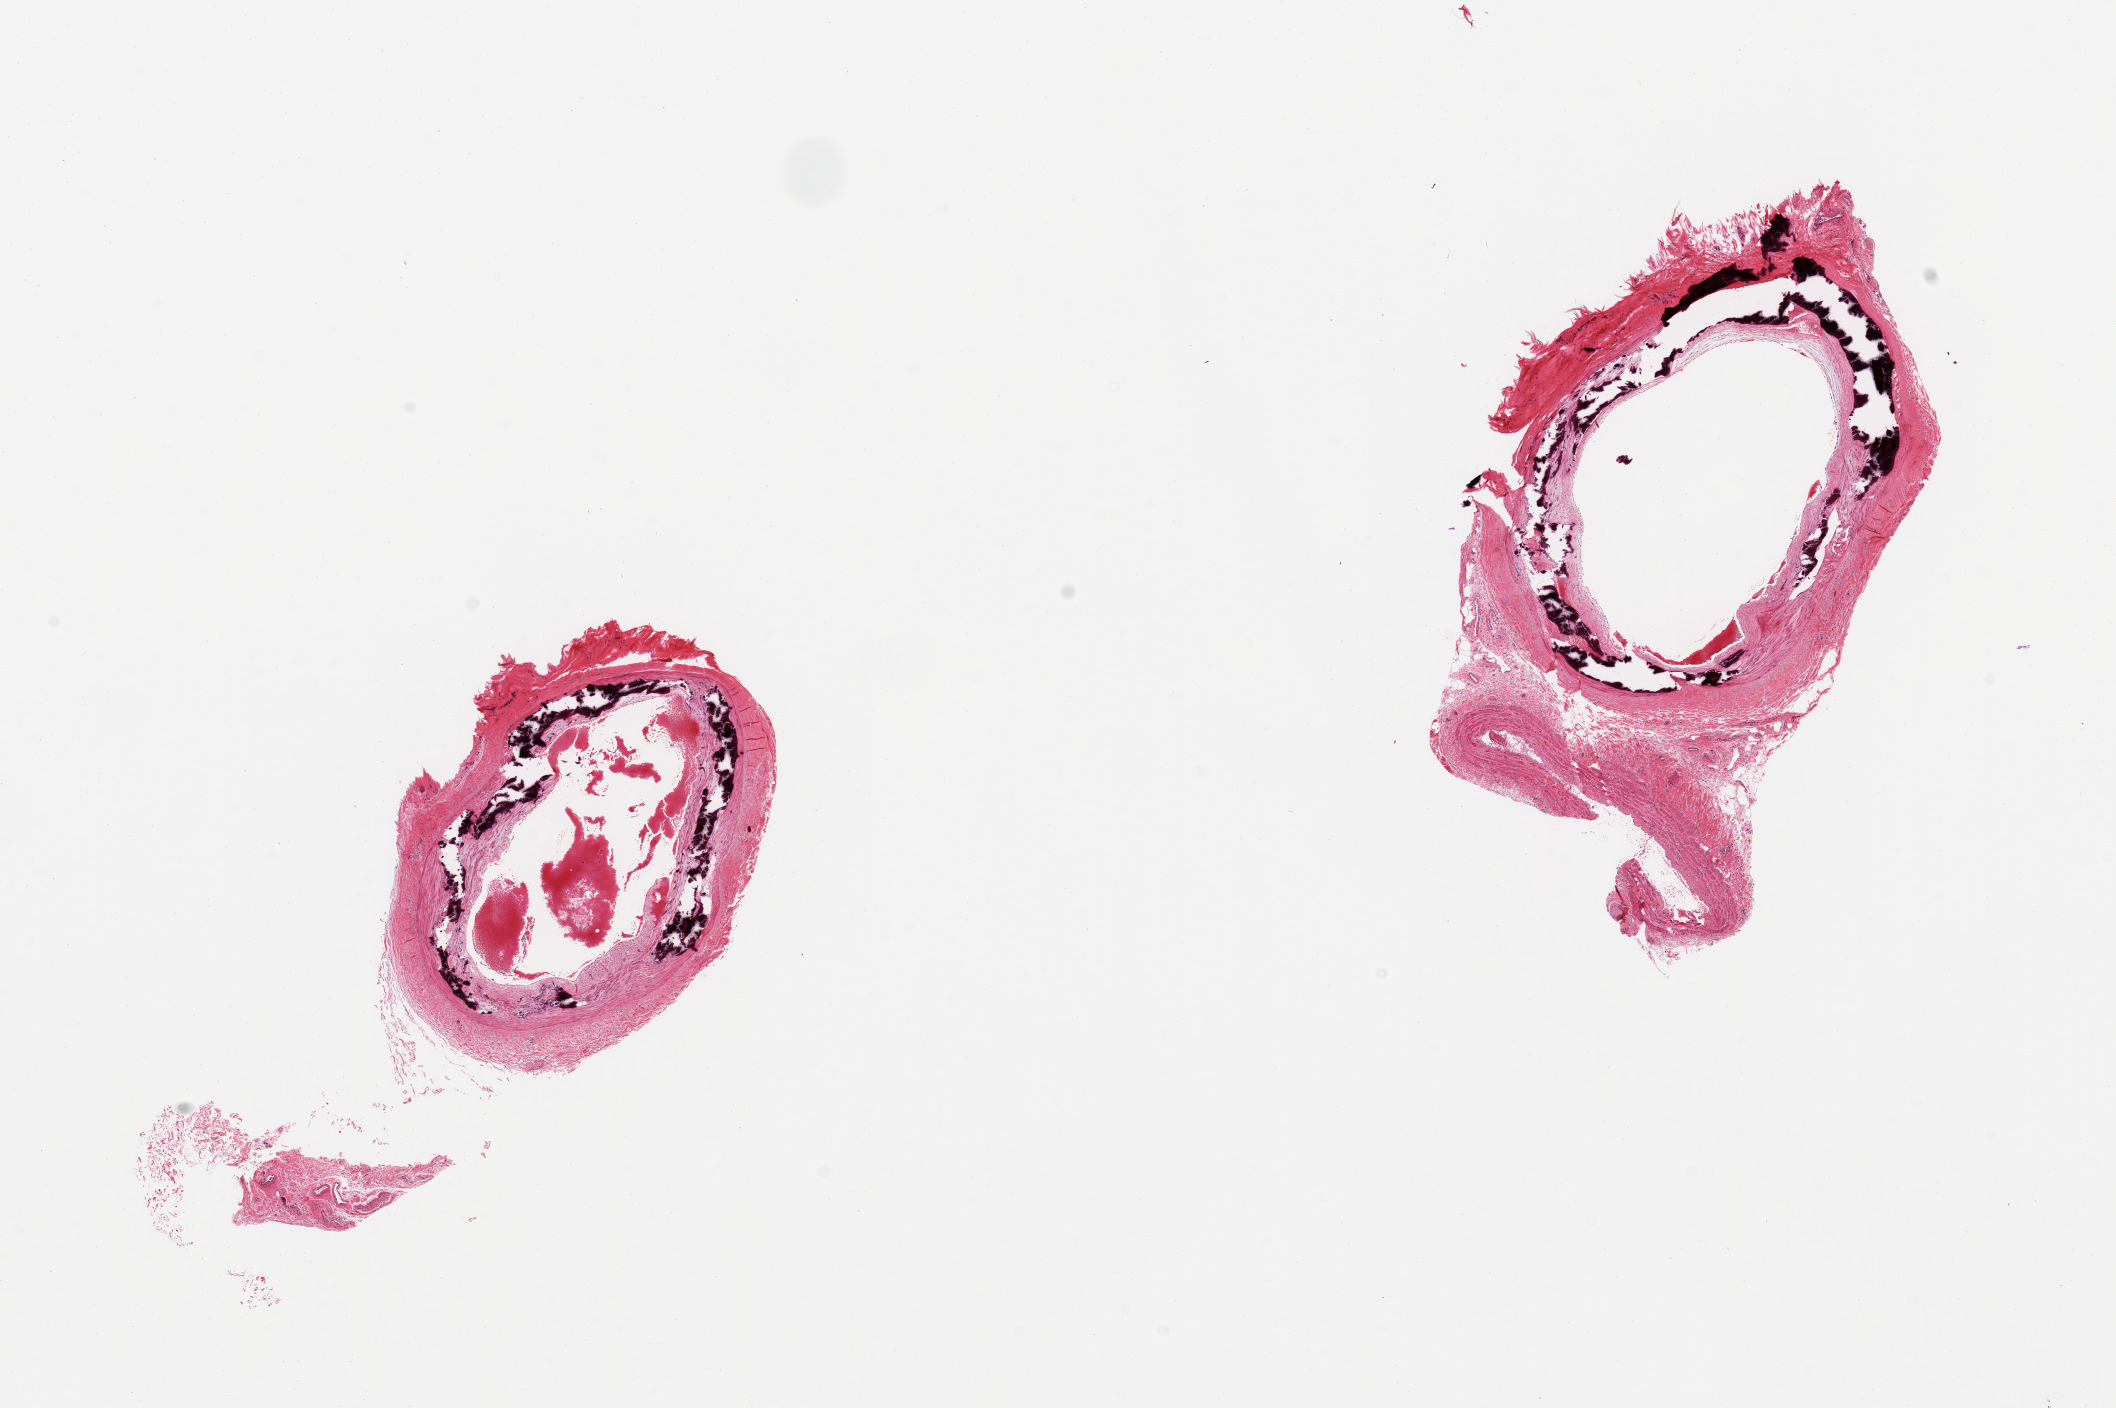
Haematoxylin and eosin whole-slide image — a low-resolution overview of the entire scanned area, about 16.7 x 11.1 mm (slide scanned at 20x), PAXgene-fixed paraffin-embedded (PFPE) section, section of tibial artery (target tissue), tissue donor sample. Donor sex: male.
Pathologist's review note for this sample: 2 pieces; extensive medial calcification.